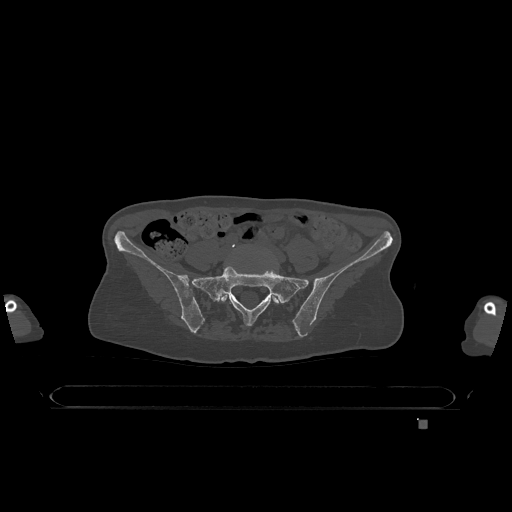
CT including the spine, one axial slice; slice 202 of 1317 in the series (ordered by position); bone window (W 1800 / L 400 HU); 512 × 512 image matrix. Patient: female, 74 years. From the clinical record (not read from this slice): primary cancer: lung; vertebrae with lytic lesions (as recorded): T1, T4, T5, T6, L4, L5.
Outlined on this slice (semi-automatically segmented with operator editing):
- L5 vertebra: box from (x=219, y=293) to (x=280, y=304) px